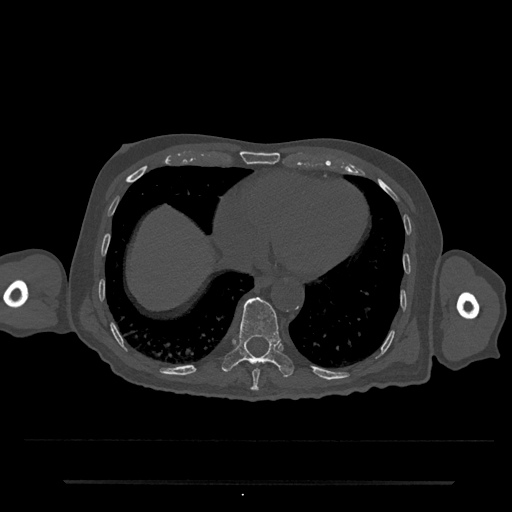
CT including the spine, one axial slice. Position 324 of 797 along the scan axis. Reconstruction kernel Br40s/3. 120 kVp. Bone window (W 1800 / L 400 HU). 512 × 512 image matrix, field of view 427 × 427 mm. Patient: male, 74 years. From the clinical record (not read from this slice): primary cancer: prostate.
Annotated regions visible in this slice (semi-automatically segmented with operator editing):
- T10 vertebra: bounding box <222,297,294,377> (left, top, right, bottom; pixels)
- T9 vertebra: <250,368,260,391>